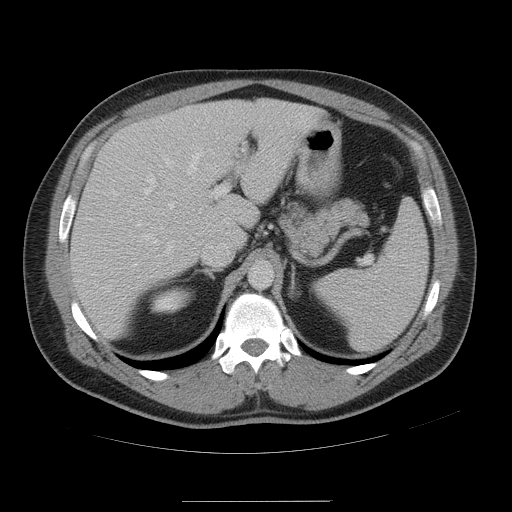
Contrast-enhanced abdominal CT, one axial slice; position 34 of 54 along the scan axis; 120 kVp; intravenous contrast given; soft-tissue window (W 400 / L 40 HU); 512 × 512 image matrix, field of view 436 × 436 mm. Male patient, age 40 years. From the clinical record (not read from this slice): diagnosis: colorectal cancer liver metastases, imaged before liver resection; multiple liver metastases: no; largest metastasis: 15 cm; disease in both lobes: no.
Annotated regions visible in this slice (outlined manually by an expert reader):
- hepatic veins: bounding box <144,150,202,254> (left, top, right, bottom; pixels)
- liver: <70,99,327,339>
- planned liver remnant (the part of the liver to remain after resection): <191,99,327,249>
- portal vein (with intrahepatic branches): <145,148,244,209>